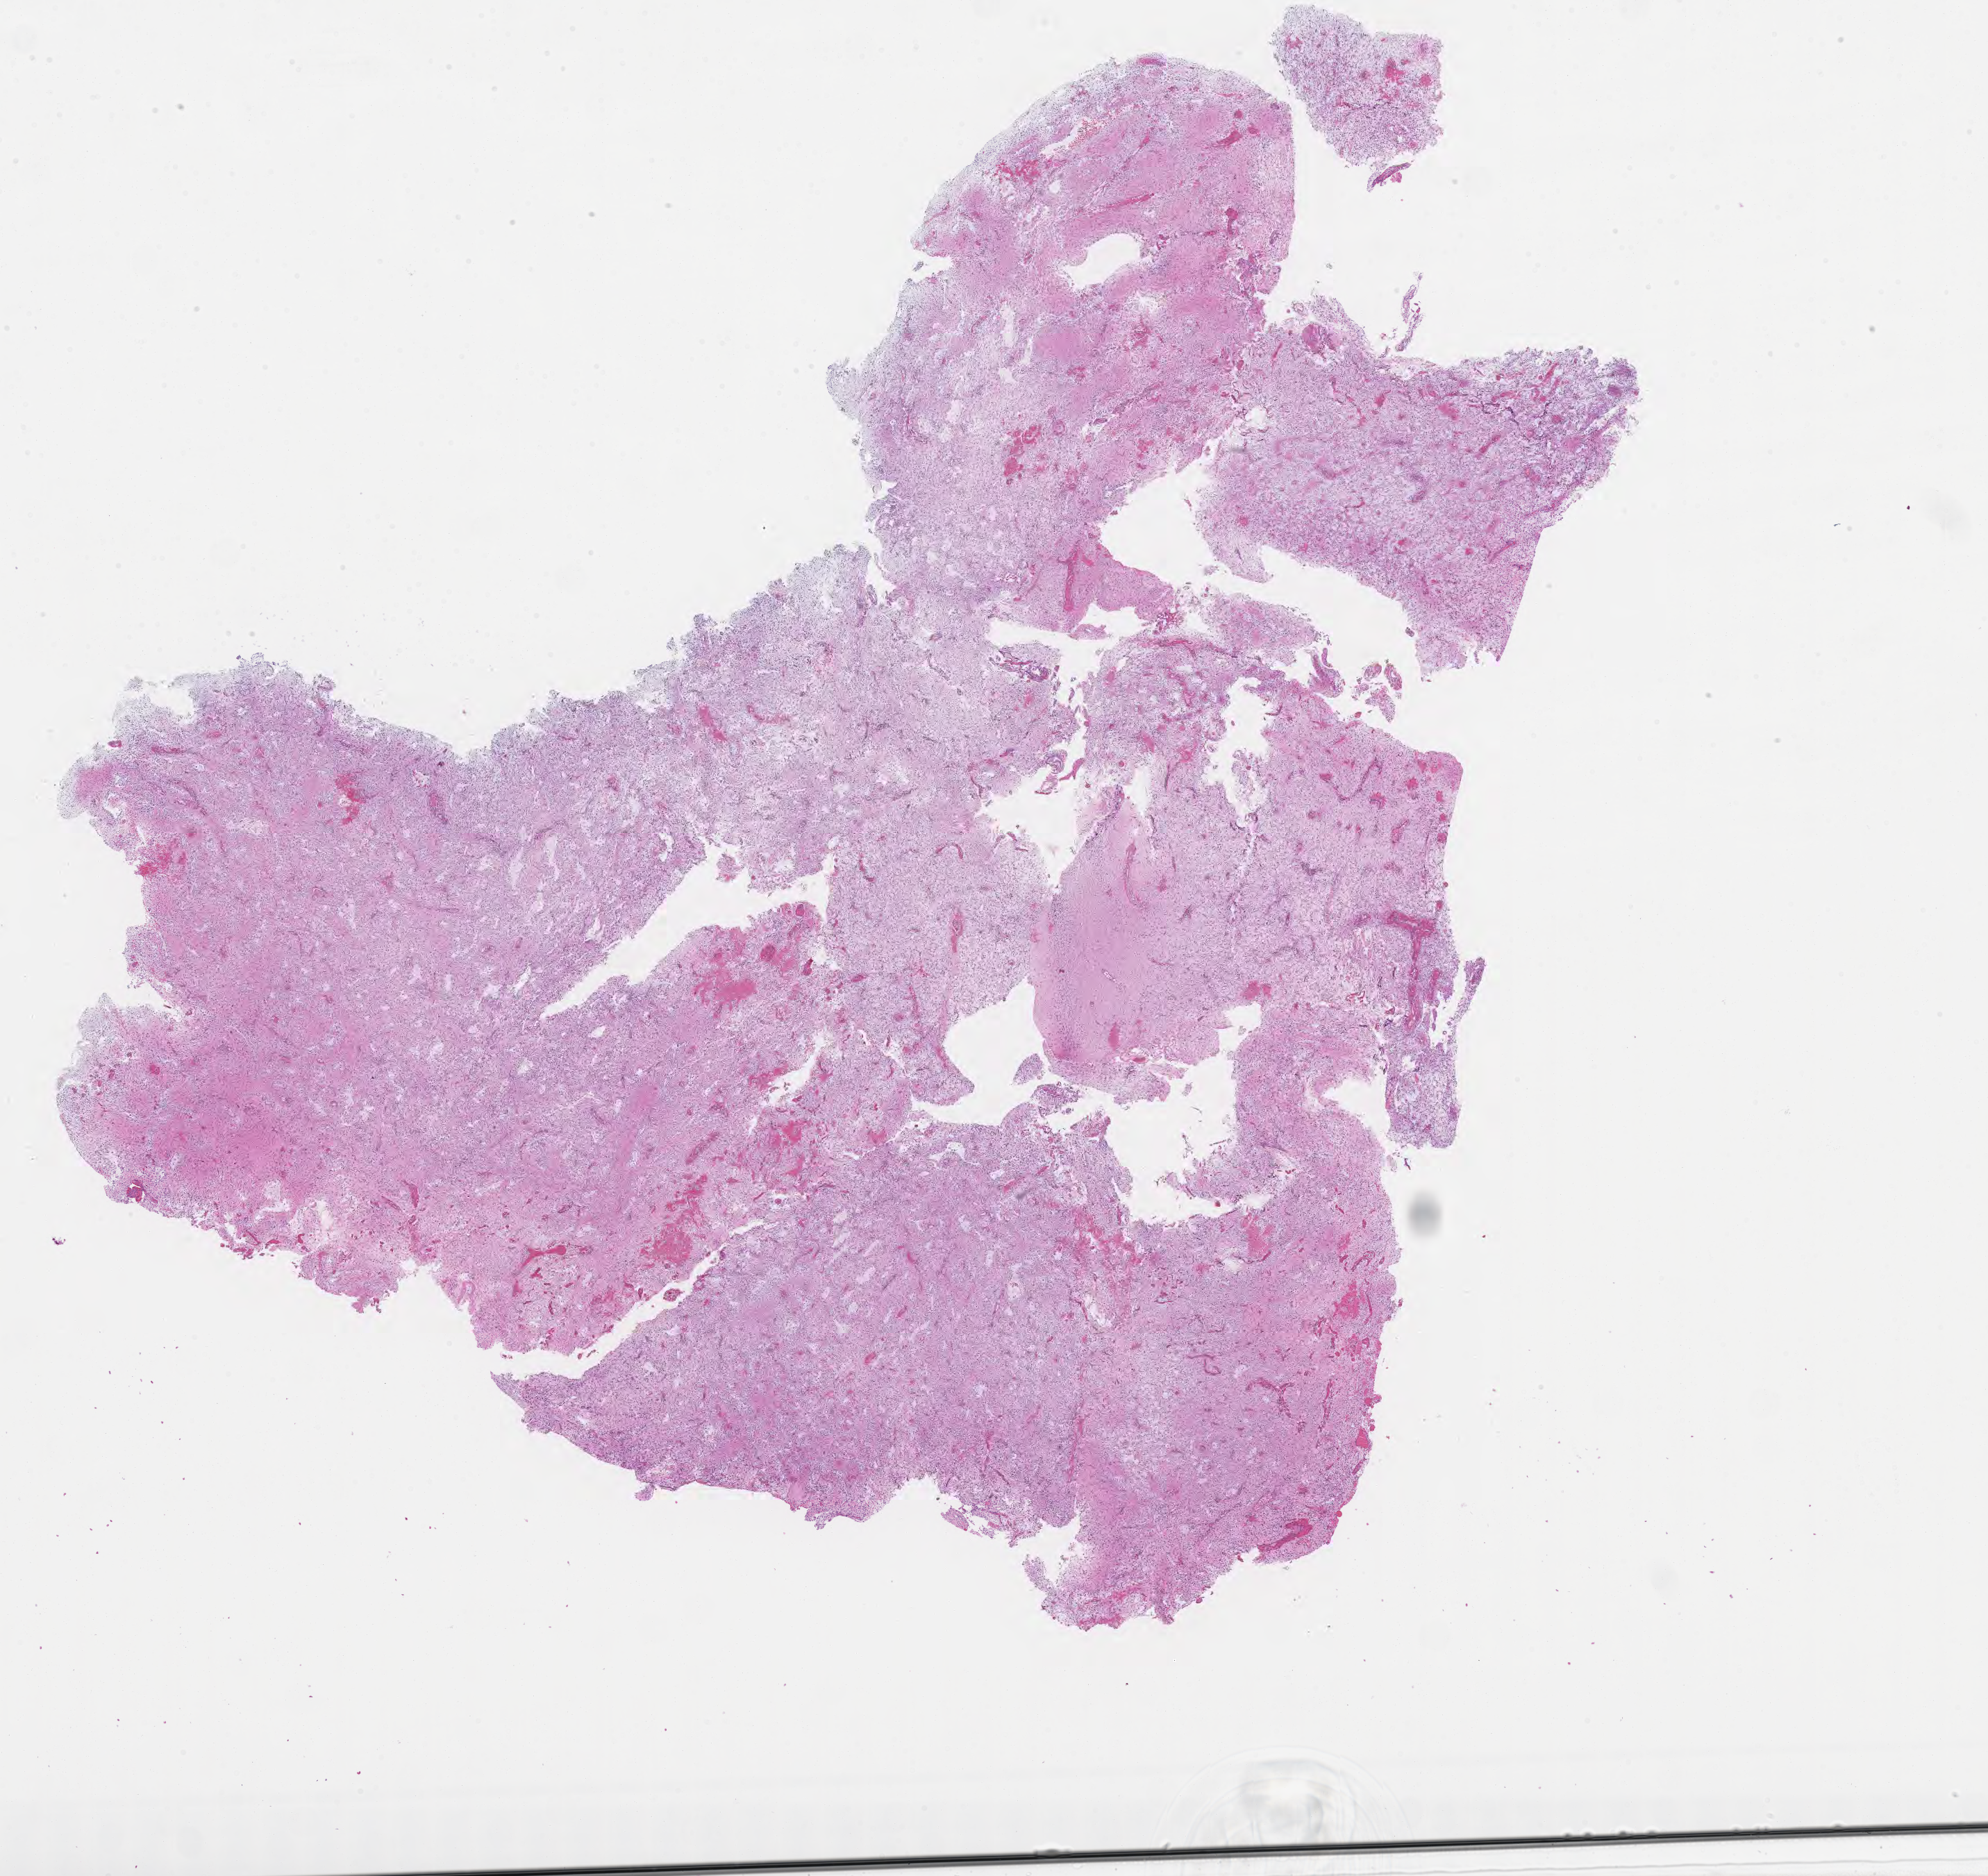
Whole-slide image, H&E stain of tumor tissue from the brain, whole scanned area (about 23.1 x 21.8 mm) shown as a low-resolution overview. Formalin-fixed, paraffin-embedded (FFPE) tissue. Male patient, age 115 months (9 years 7 months).
Diagnosis: Pilocytic astrocytoma.